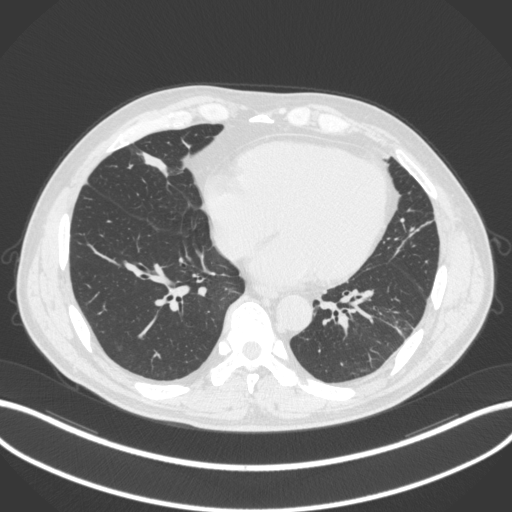
Chest CT, one axial slice. Slice 92 of 399 in the series (ordered by position). Reconstruction kernel B31f. Lung window (W 1500 / L -600 HU). 1 mm slice thickness. 512 × 512 image matrix. Male patient, age 59 years. Case-level facts recorded for this patient, not image findings: clinical TNM (as recorded): T2a N1 M0.
Outlined on this slice (bounding box drawn by a radiologist):
- lung tumour (recorded histology: adenocarcinoma): box from (x=133, y=145) to (x=179, y=189) px